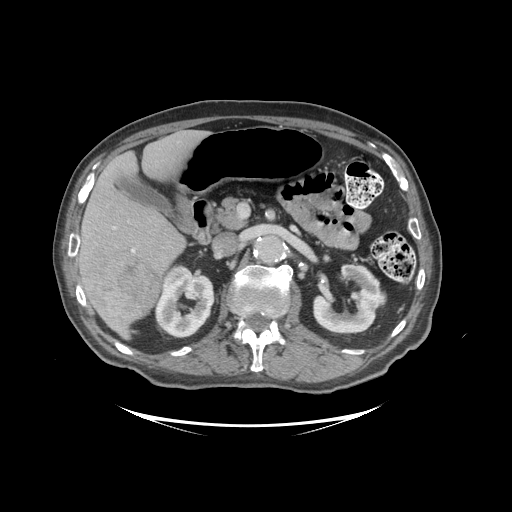
Contrast-enhanced abdominal CT (liver protocol), one axial slice. Position 51 of 99 along the scan axis. Reconstruction kernel STANDARD. Soft-tissue window (W 400 / L 40 HU). 2.5 mm slice thickness. 512 × 512 image matrix. Case-level facts recorded for this patient, not image findings: diagnosis: hepatocellular carcinoma (patient treated with transarterial chemoembolisation; whether this scan precedes or follows treatment is not stated here); TNM stage (as recorded): Stage-I; Child-Pugh class: A; tumour differentiation: moderately differentiated; tumour nodularity: uninodular.
Structures marked on this image (semi-automatically segmented with operator editing):
- liver parenchyma outside the tumour (the mass and vessels are separate outlines, so this box may not span the whole liver): bounding box (x1, y1, x2, y2) in pixels: (74, 130, 207, 336)
- mass: (88, 259, 161, 322)
- liver vessels: (76, 227, 135, 252)